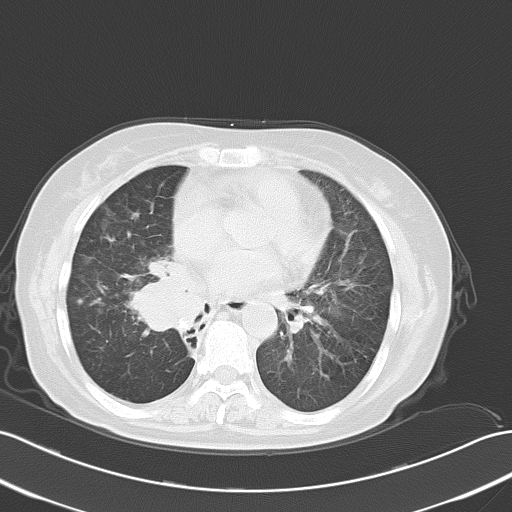
Chest CT, one axial slice; slice 32 of 62 in the series (ordered by position); reconstruction kernel B70f; 120 kVp; lung window (W 1500 / L -600 HU); 5 mm slice thickness; 512 × 512 image matrix. Patient: female, 65 years. From the clinical record (not read from this slice): clinical TNM (as recorded): T1c N3 M0.
Outlined on this slice (rectangle marked by the reading radiologist):
- lung tumour (recorded histology: small cell carcinoma): bounding box (x1, y1, x2, y2) in pixels: (131, 250, 201, 343)